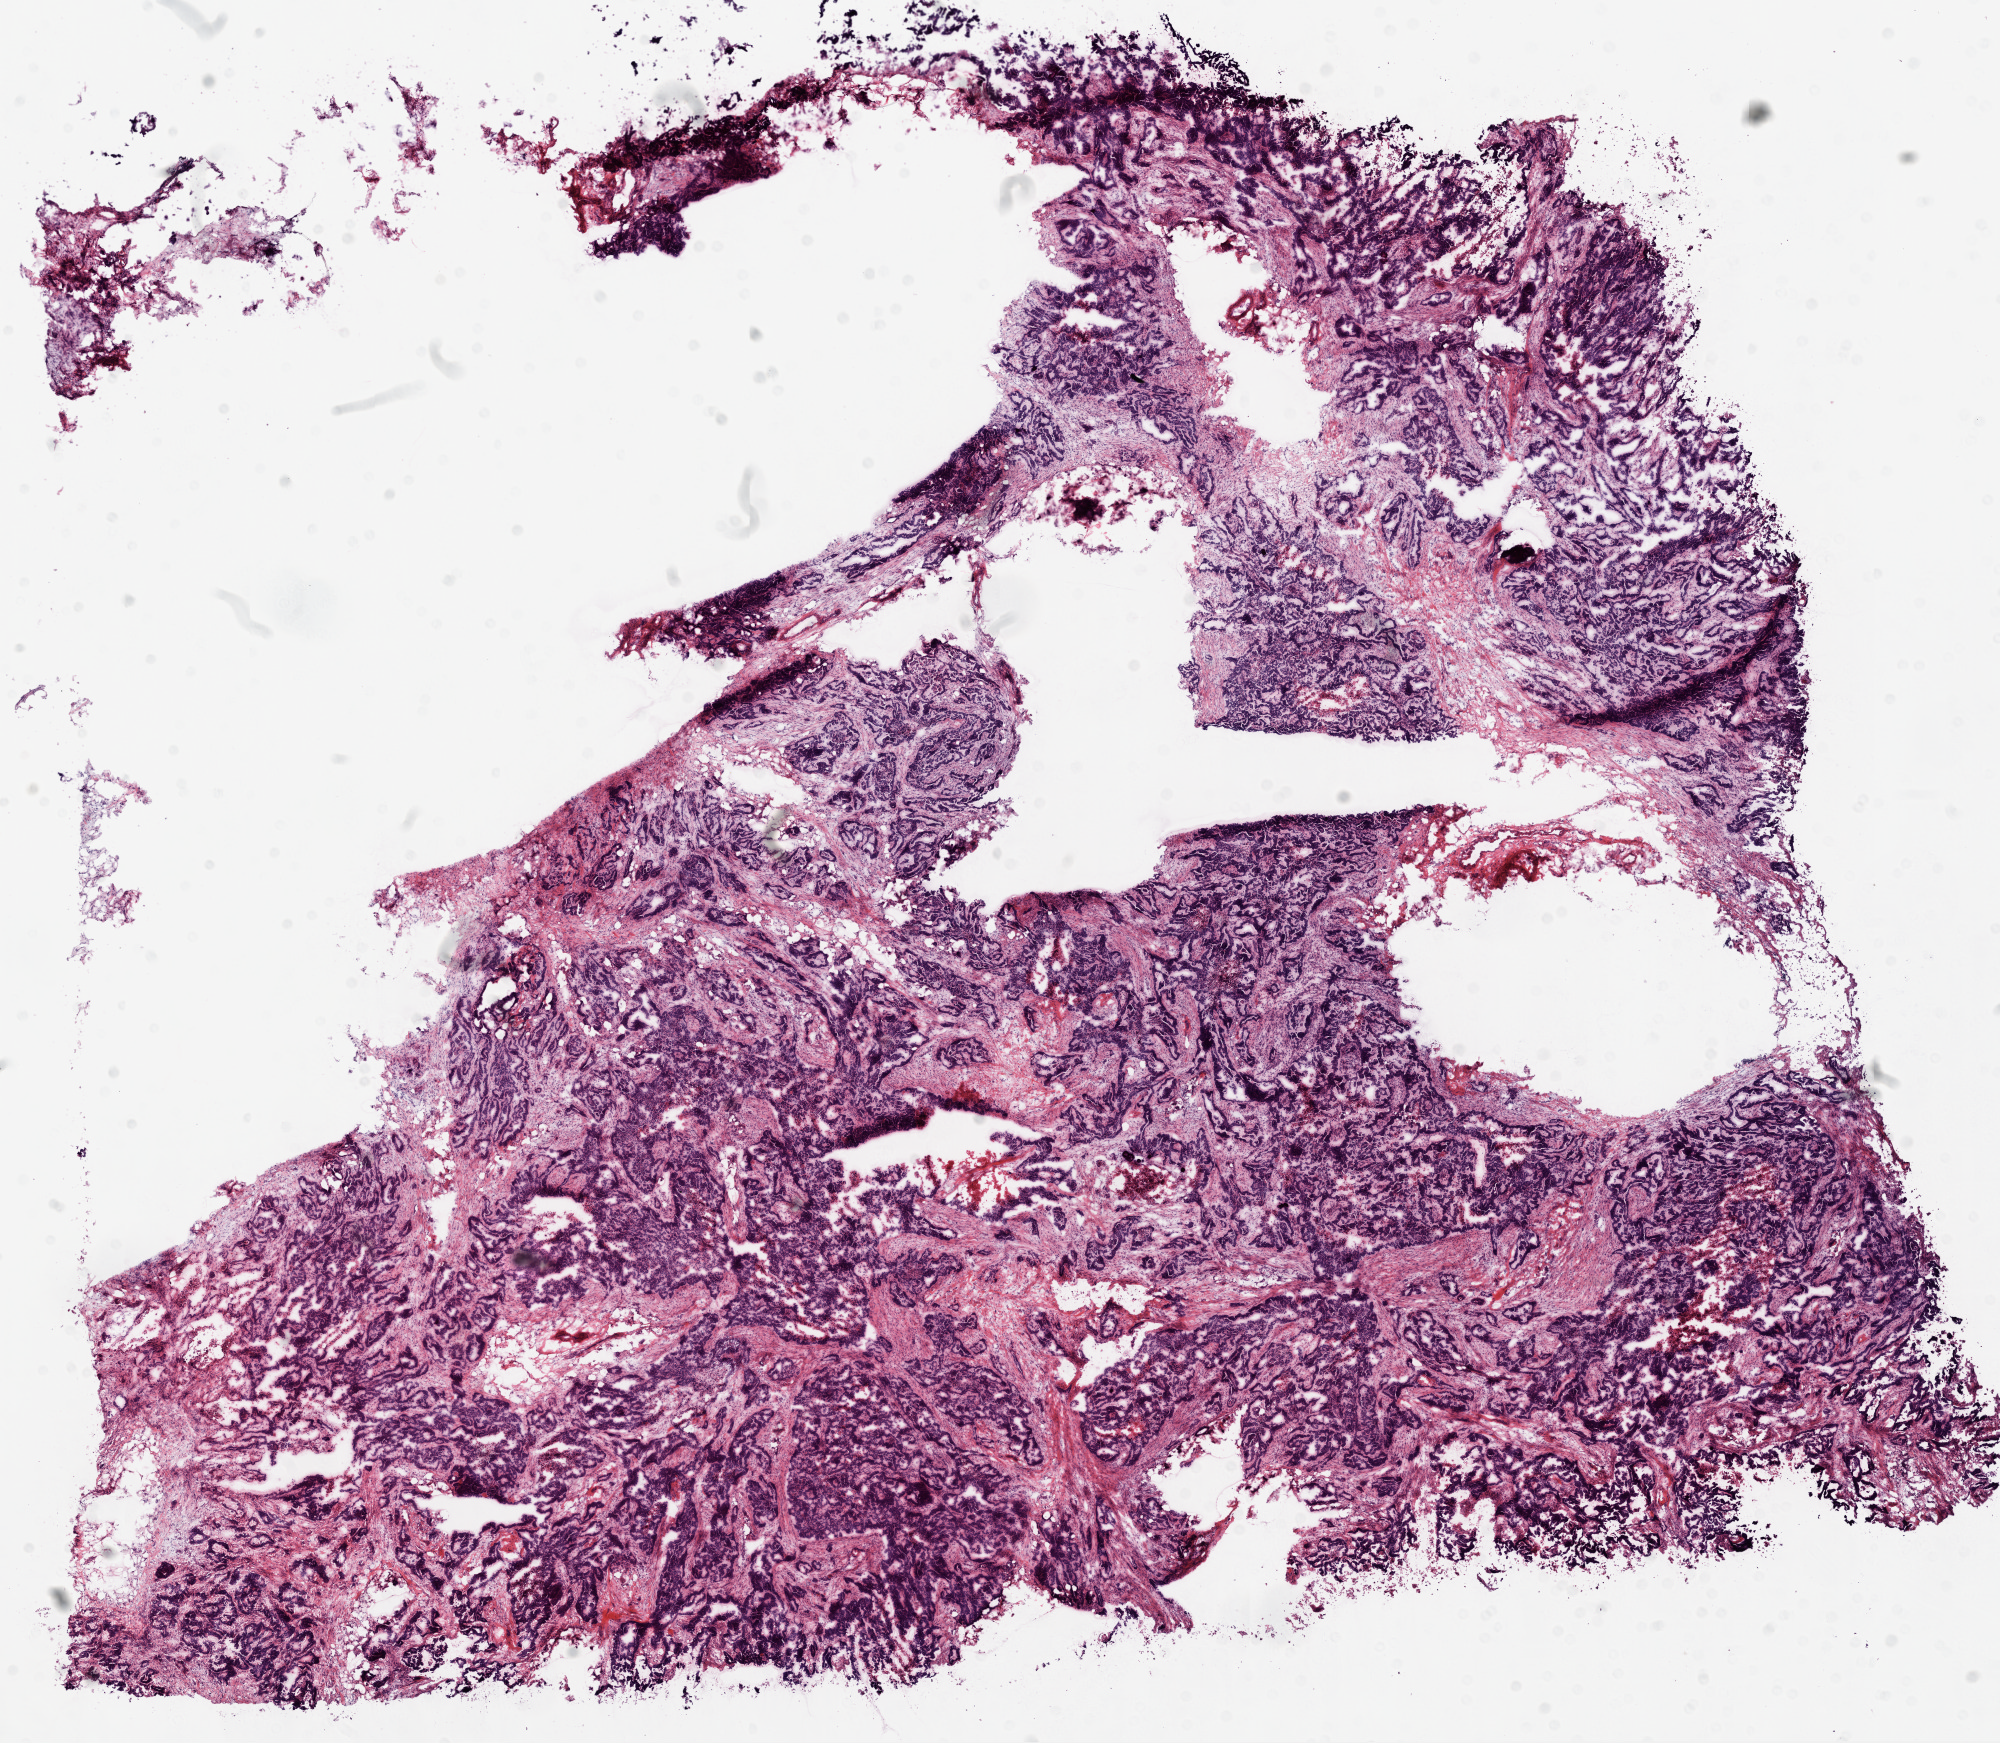
H&E whole-slide image, shown as a low-resolution overview of the whole scanned area (about 16.0 x 14.0 mm, acquisition: 20x scan); frozen section; ovary, primary tumour sample. Female patient; age at initial diagnosis 74 years. Histologic grade: GX (grade cannot be assessed). Composition of this section per pathologist review: tumour cells 80%, tumour nuclei 90%, normal cells 0%, stromal cells 15%, necrosis 5%.
FIGO stage: IV. Histologic diagnosis: Serous cystadenocarcinoma, NOS.